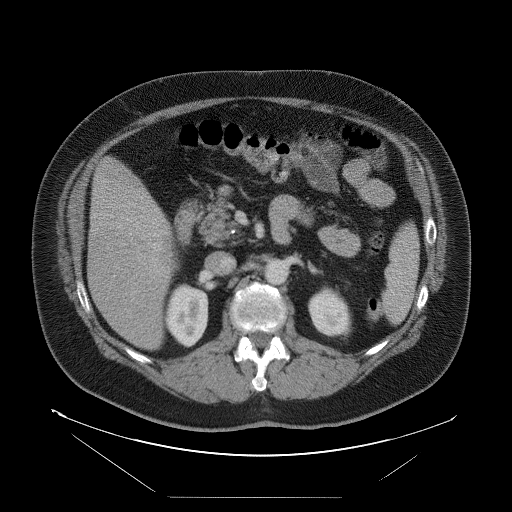
Contrast-enhanced abdominal CT, one axial slice; slice 42 of 114 in the series (ordered by position); 120 kVp; intravenous contrast given; soft-tissue window (W 400 / L 40 HU); 5 mm slice thickness; 512 × 512 image matrix. Male patient, age 61 years. Case-level facts recorded for this patient, not image findings: diagnosis: colorectal cancer liver metastases, imaged before liver resection; multiple liver metastases: no; largest metastasis: 6.5 cm.
Annotated regions visible in this slice (manually delineated by an expert):
- liver: bounding box <89,159,176,350> (left, top, right, bottom; pixels)
- liver metastasis: <170,249,176,268>